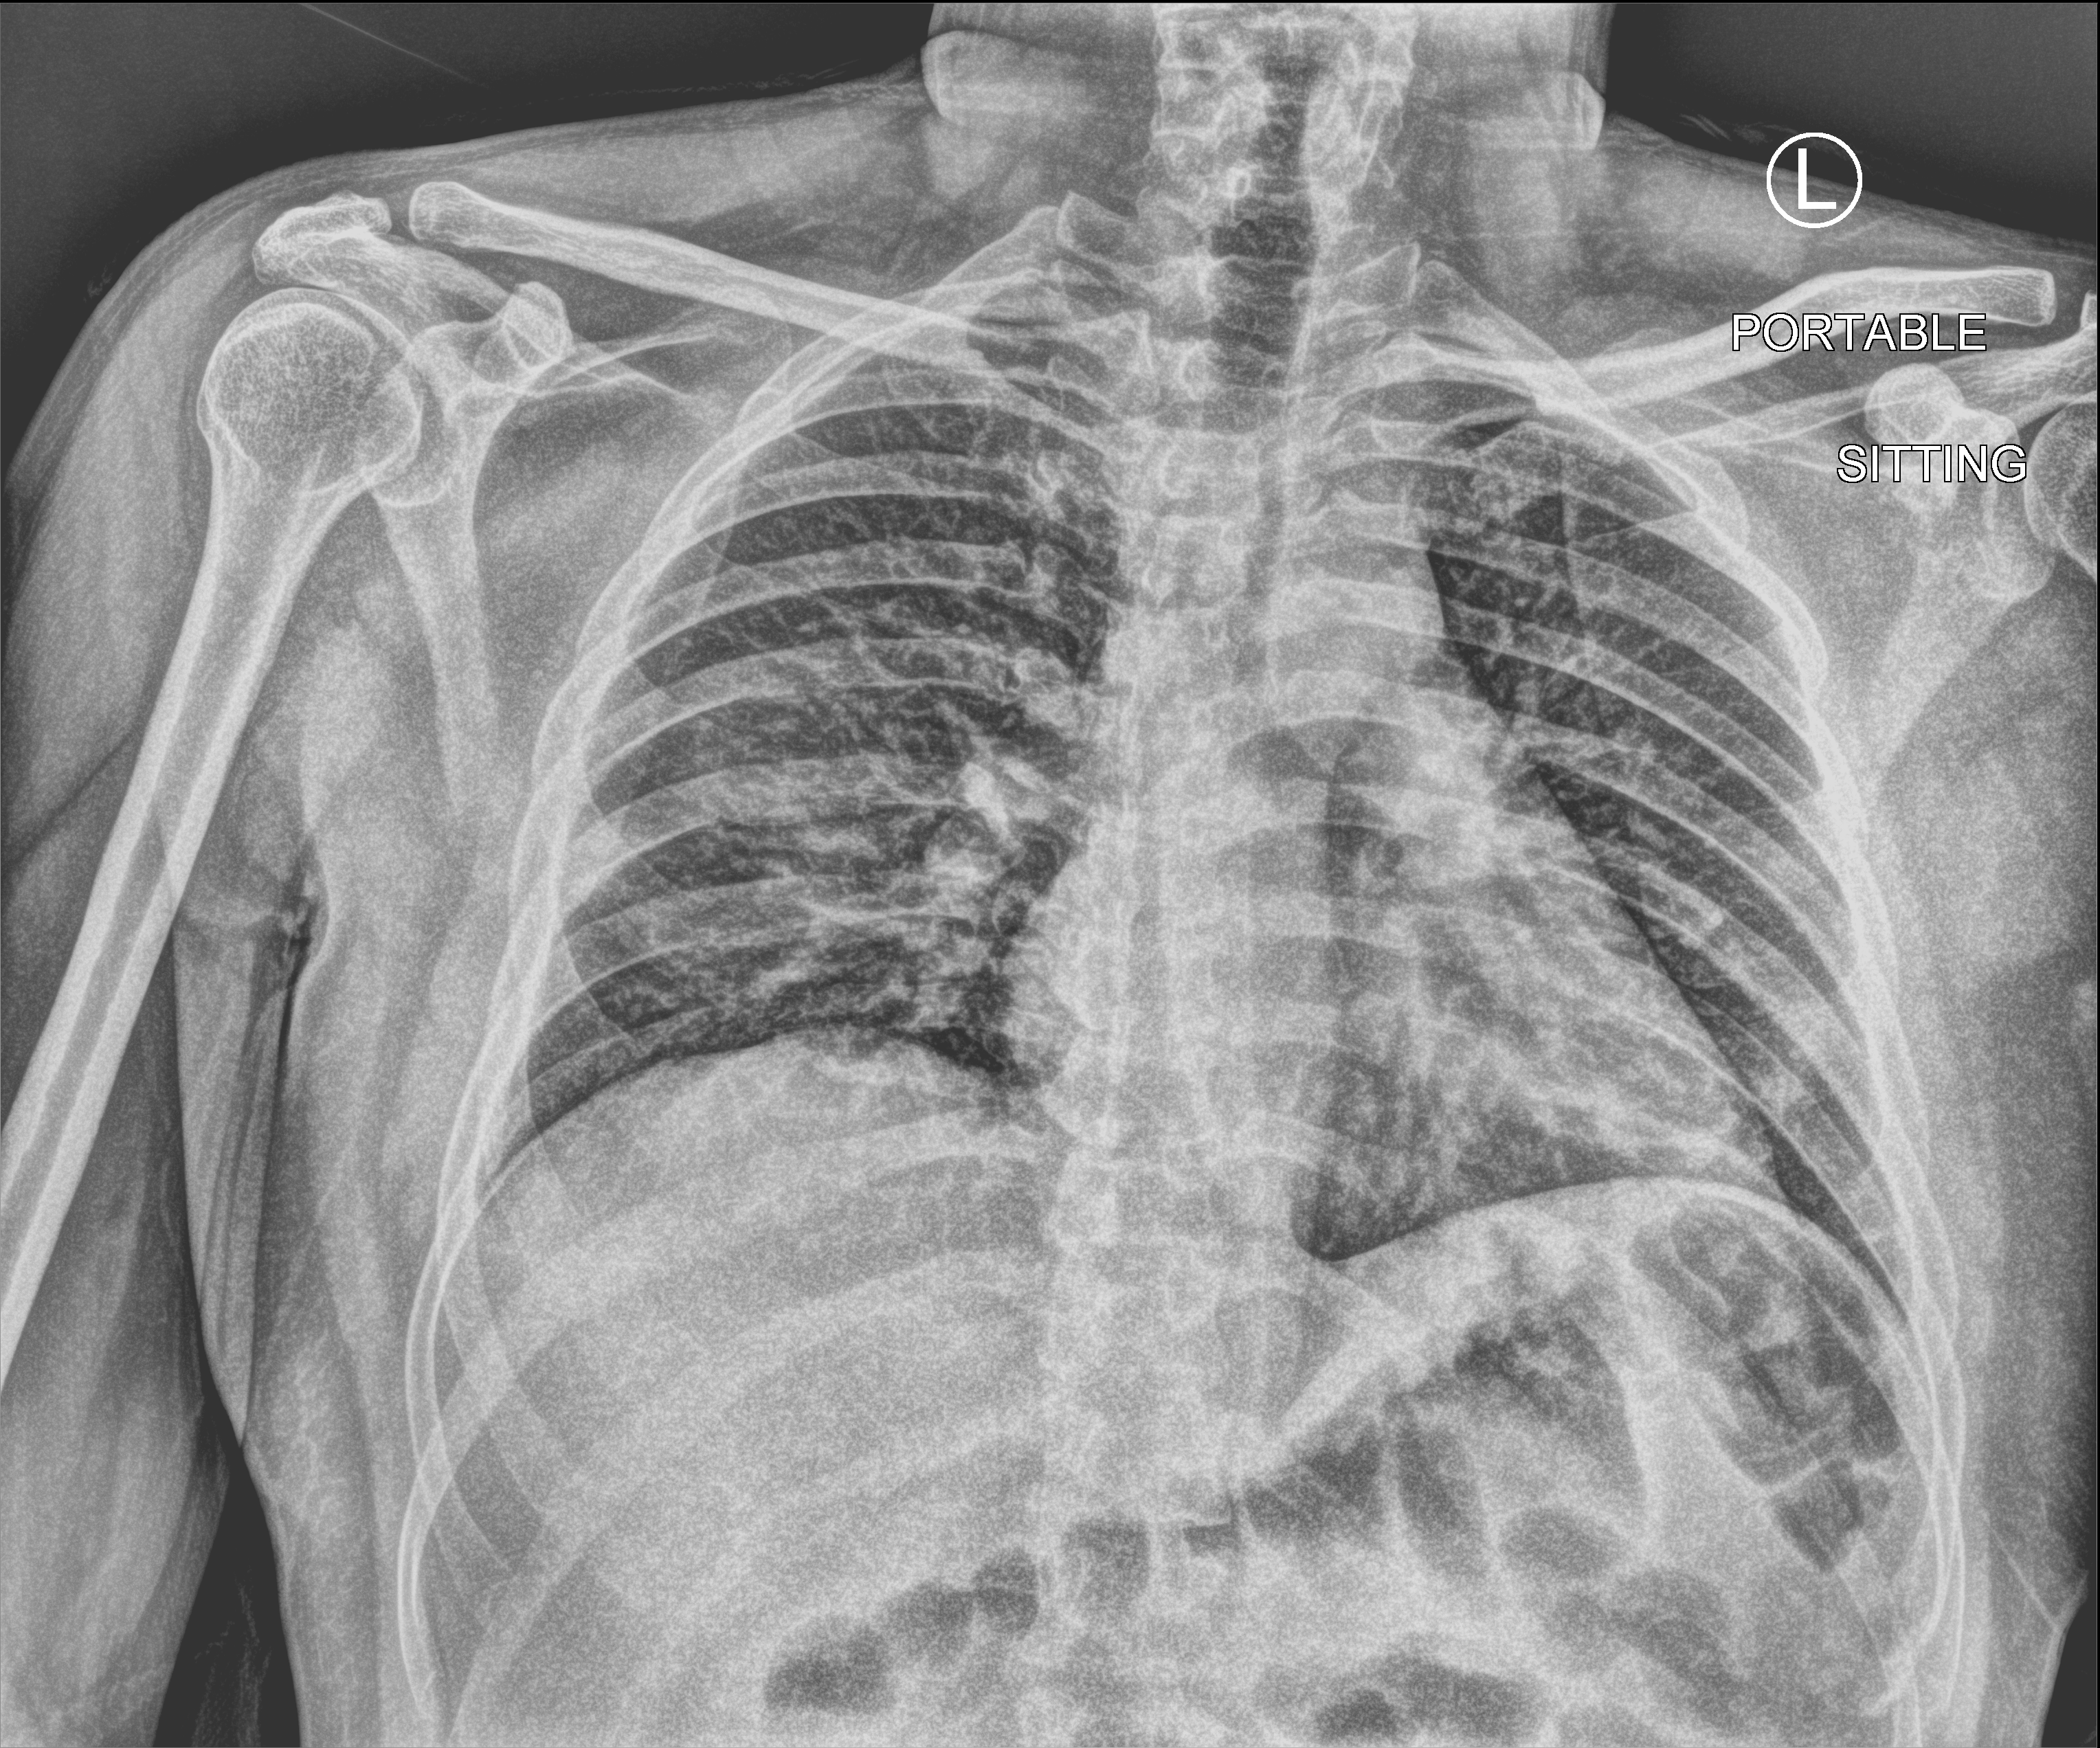
Bedside chest radiograph (computed radiography). Patient hospitalised with COVID-19; male, aged 18–59 years.
From the hospital-stay record, not from the radiograph (when in the stay this image was taken is not recorded): length of hospital stay: 1 day; other chronic lung disease (admission record): no; COPD (admission record): no.